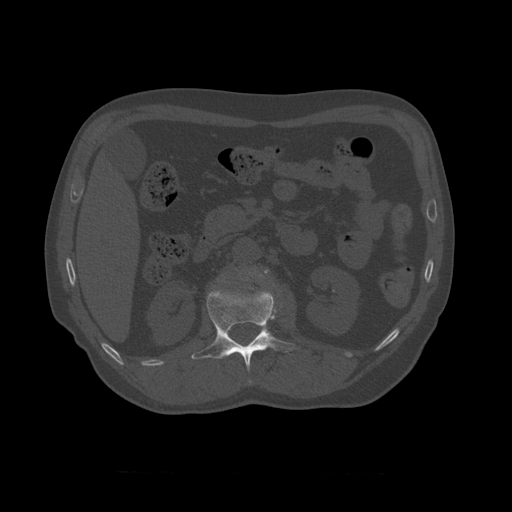
CT including the spine, one axial slice. Slice 352 of 450 in the series (ordered by position). 120 kVp. Bone window (W 1800 / L 400 HU). 512 × 512 image matrix. Patient age 75 years. Case-level facts recorded for this patient, not image findings: primary cancer: prostate.
Structures marked on this image (semi-automatic segmentation, software-assisted and operator-edited):
- L1 vertebra: bounding box <191,284,294,384> (left, top, right, bottom; pixels)
- L2 vertebra: <241,268,270,288>